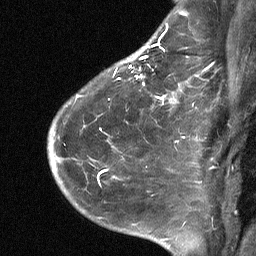
Breast MRI (dynamic contrast-enhanced), one sagittal slice; slice 47 of 64 in the series (ordered by position); dynamic contrast-enhanced study with each time point stored as its own series, time point 2 of 3 at this slice position (early post-contrast, ordered by acquisition time); 1.5 T; TE 4.8 ms, TR 27 ms; 2 mm slice thickness; 256 × 256 image matrix. Female patient, age 51 years. Case-level facts recorded for this patient, not image findings: setting: breast cancer imaged before/during neoadjuvant chemotherapy; receptor status: HR-positive, HER2-negative.
Outlined on this slice (semi-automatic segmentation, software-assisted and operator-edited):
- analysis volume of interest (the breast-tissue region the enhancement analysis was run in; not a lesion): bounding box <72,34,182,118> (left, top, right, bottom; pixels)
- tumour enhancement mask (voxels above the 90 % enhancement threshold inside the analysis volume of interest): <119,34,164,101>